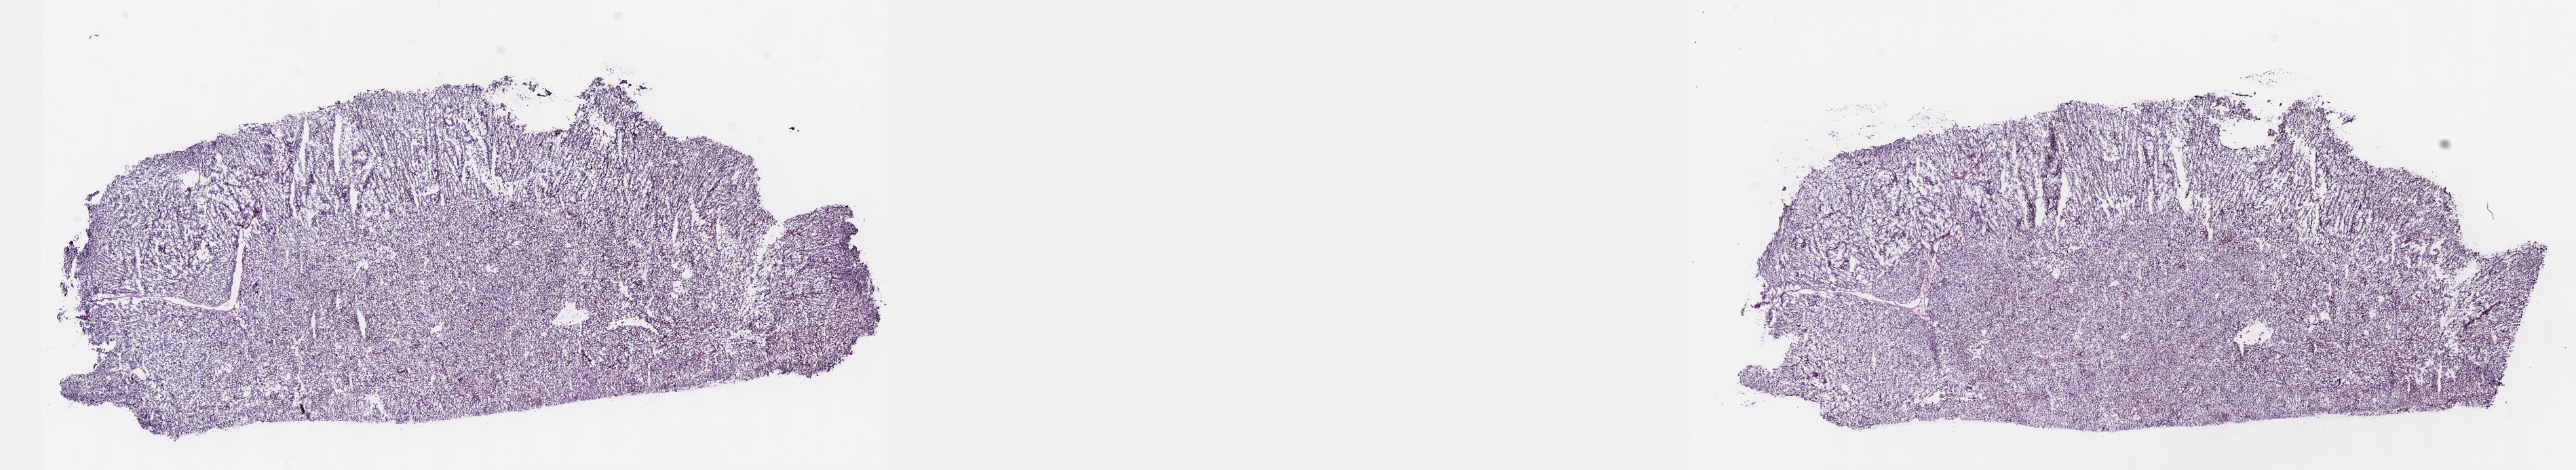
Digitized H&E-stained tissue section (whole slide) — low-resolution overview of the scanned area, about 30.7 x 5.6 mm (slide scanned at 40x). Frozen section. Metastatic tumour sample, sampled site: pelvic lymph nodes. Female patient; age at initial diagnosis 68 years. Pathologist review of this section (percent, as recorded): tumour cells 100%, tumour nuclei 80%, normal cells 0%, stromal cells 0%, necrosis 0%. Inflammatory infiltration, as recorded: lymphocyte infiltration 2%, monocyte infiltration 0%, neutrophil infiltration 0%.
This section: metastatic tumour tissue. Patient diagnosis: Malignant melanoma, NOS.